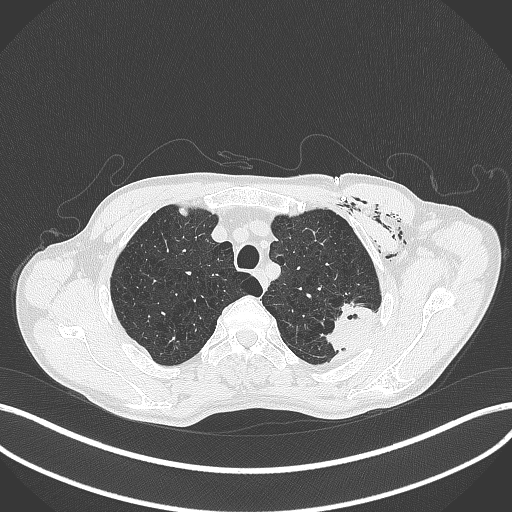
Chest CT, one axial slice. Position 342 of 457 along the scan axis. 120 kVp. Lung window (W 1500 / L -600 HU). 512 × 512 image matrix. Patient: male, 58 years. From the clinical record (not read from this slice): clinical TNM (as recorded): T3 N0 M0.
Structures marked on this image (rectangle marked by the reading radiologist):
- lung tumour (recorded histology: adenocarcinoma): bounding box <319,300,379,351> (left, top, right, bottom; pixels)